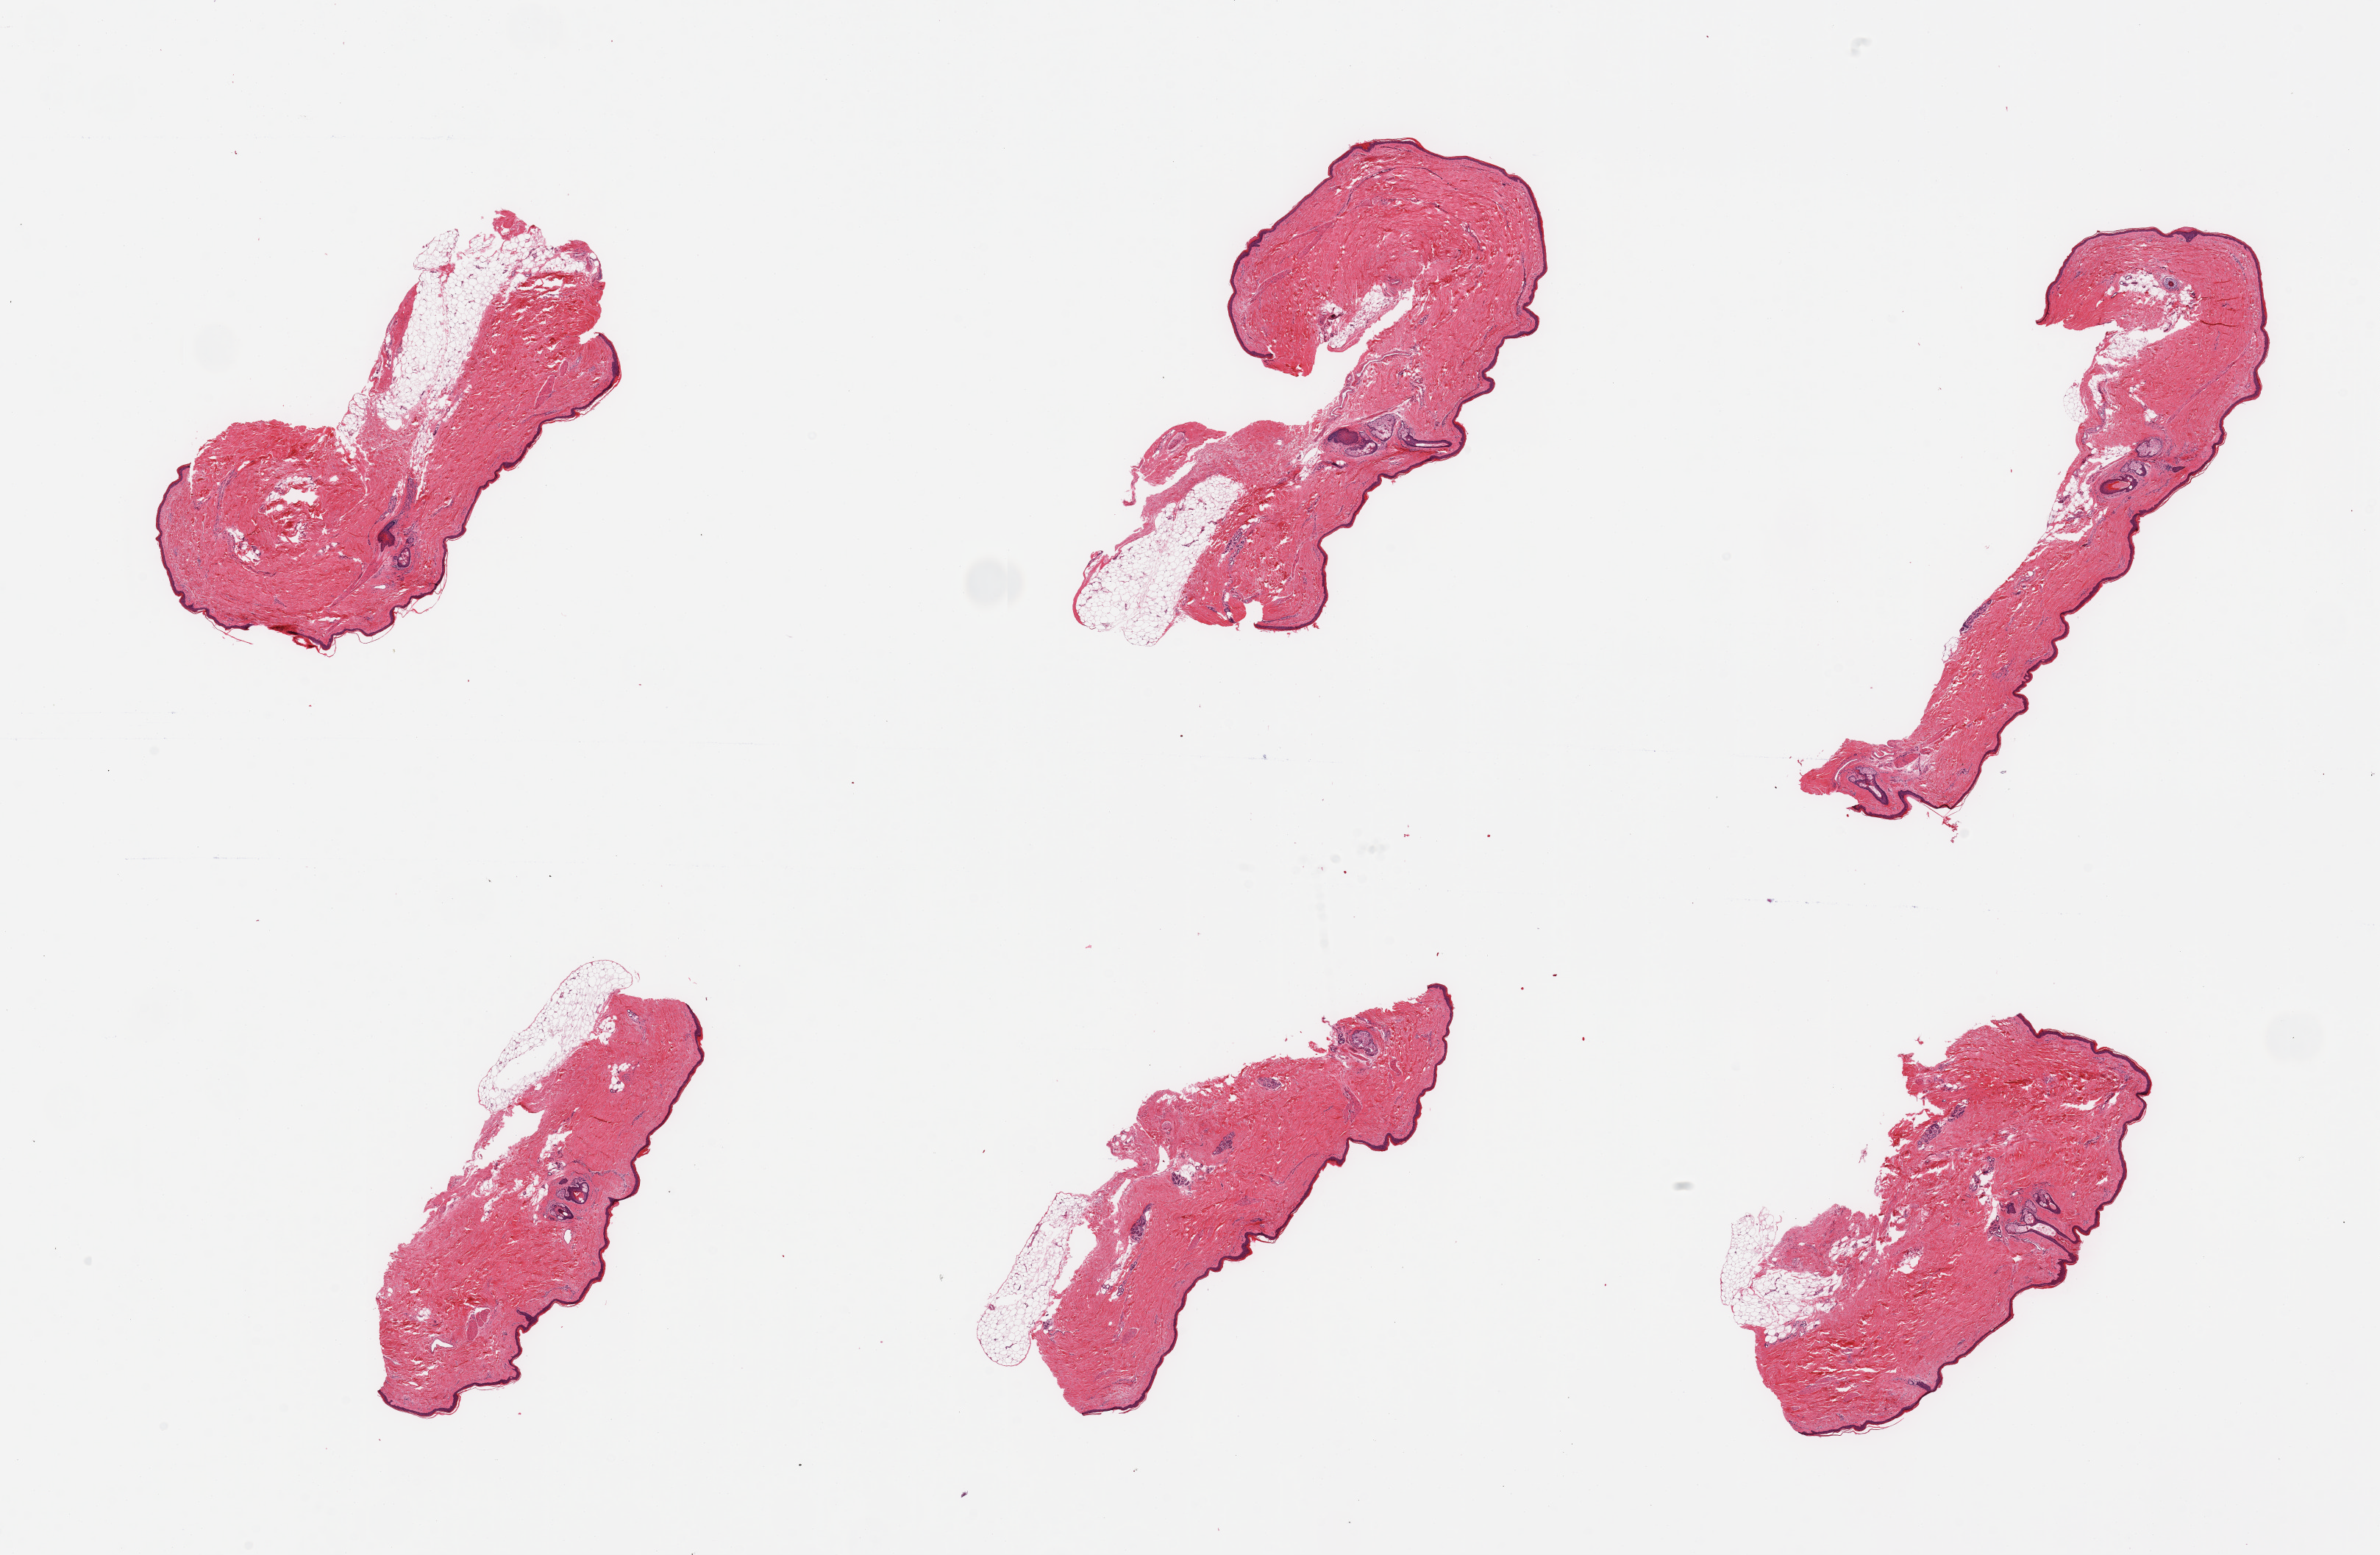
Haematoxylin and eosin whole-slide image, brightfield — low-resolution overview of the scanned area, about 25.6 x 16.7 mm (acquisition: 20x scan). PAXgene-fixed, paraffin-embedded tissue. Sampled site (target tissue): skin of lower leg. Tissue donor sample. Donor: male.
Review note (as recorded): 6 pieces; up to 20% dermal/subcutaneous fat.